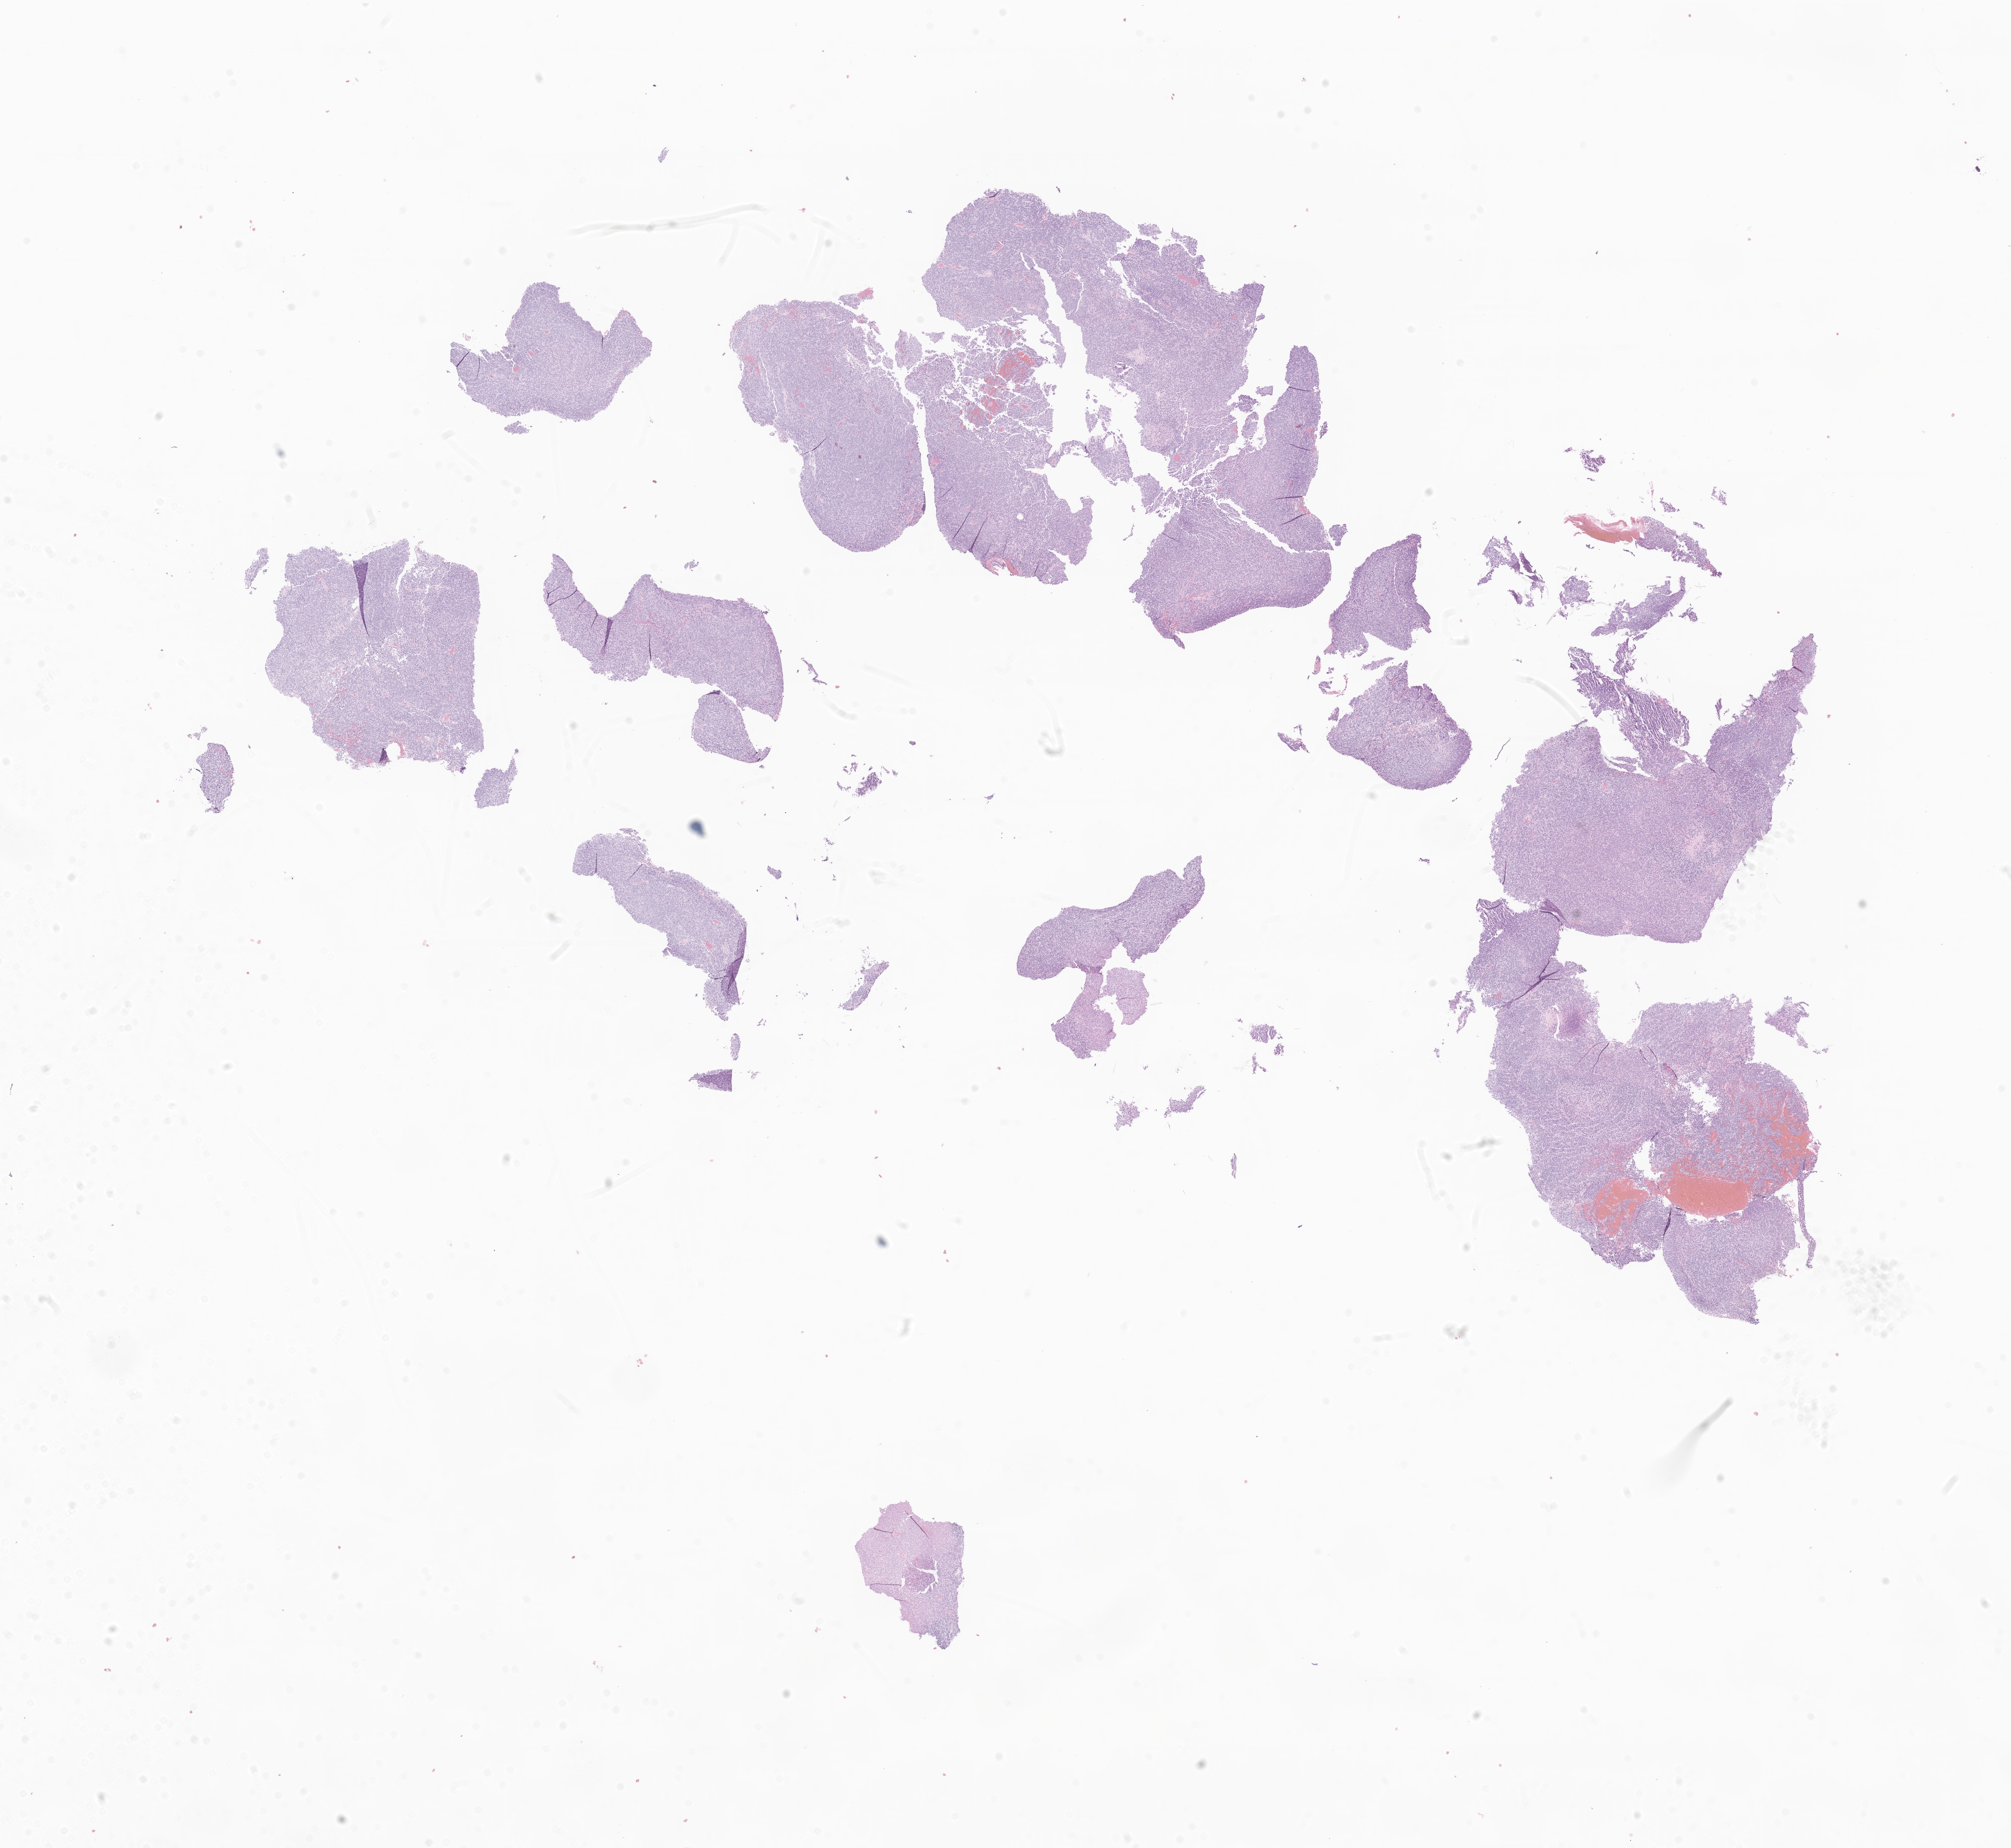
Haematoxylin and eosin whole-slide image of tumor tissue from the brain stem — a low-resolution overview of the entire scanned area, about 20.2 x 18.6 mm. Formalin-fixed paraffin-embedded section. Patient: female, age 76 months (6 years 4 months).
• diagnosis (ICD-O-3 morphology term): Medulloblastoma, NOS